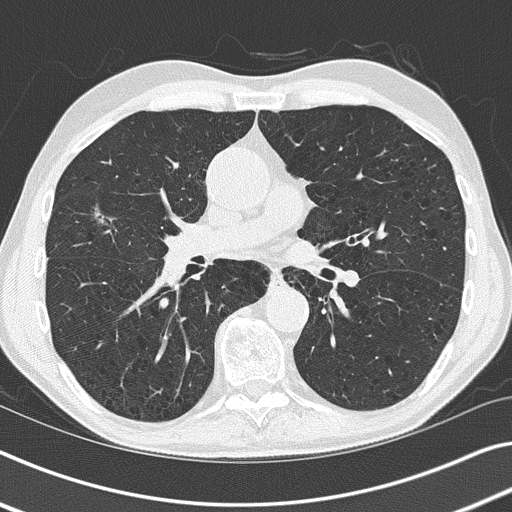
Low-dose screening chest CT, axial slice; baseline screening round; lung window (W 1500 / L -600 HU); 2 mm slice thickness; slice 76 of 155 in the series. Male, age 73 years at enrolment. Current smoker at enrolment.
Lesion marked by an expert reader, bounding box [x1, y1, x2, y2] px = [73, 193, 128, 245]. The screening reader recorded 3 non-calcified nodules or masses ≥4 mm on this exam (right upper lobe, right middle lobe, right upper lobe); which of them this box marks is not recorded. Official screen result: positive, change unspecified: nodule(s) >= 4 mm or enlarging nodule(s), mass(es), or other non-specific abnormalities suspicious for lung cancer. Lung cancer was diagnosed 45 days after this screen: bronchiolo-alveolar adenocarcinoma, NOS, right middle lobe, well differentiated (G1), stage IA (AJCC 6th edition), 11 mm at pathology.